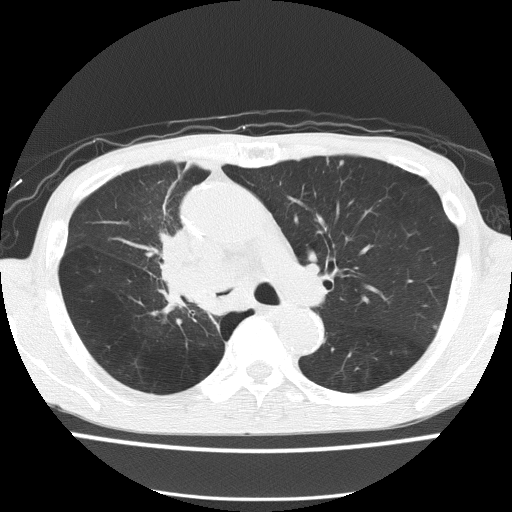
Low-dose screening chest CT, one axial slice. Lung window (W 1500 / L -600 HU). 512 × 512 image matrix, field of view 336 × 336 mm.
Structures marked on this image (manually delineated by an expert):
- lesion 1 (tumor, hilum of right lung): box from (x=165, y=229) to (x=229, y=315) px